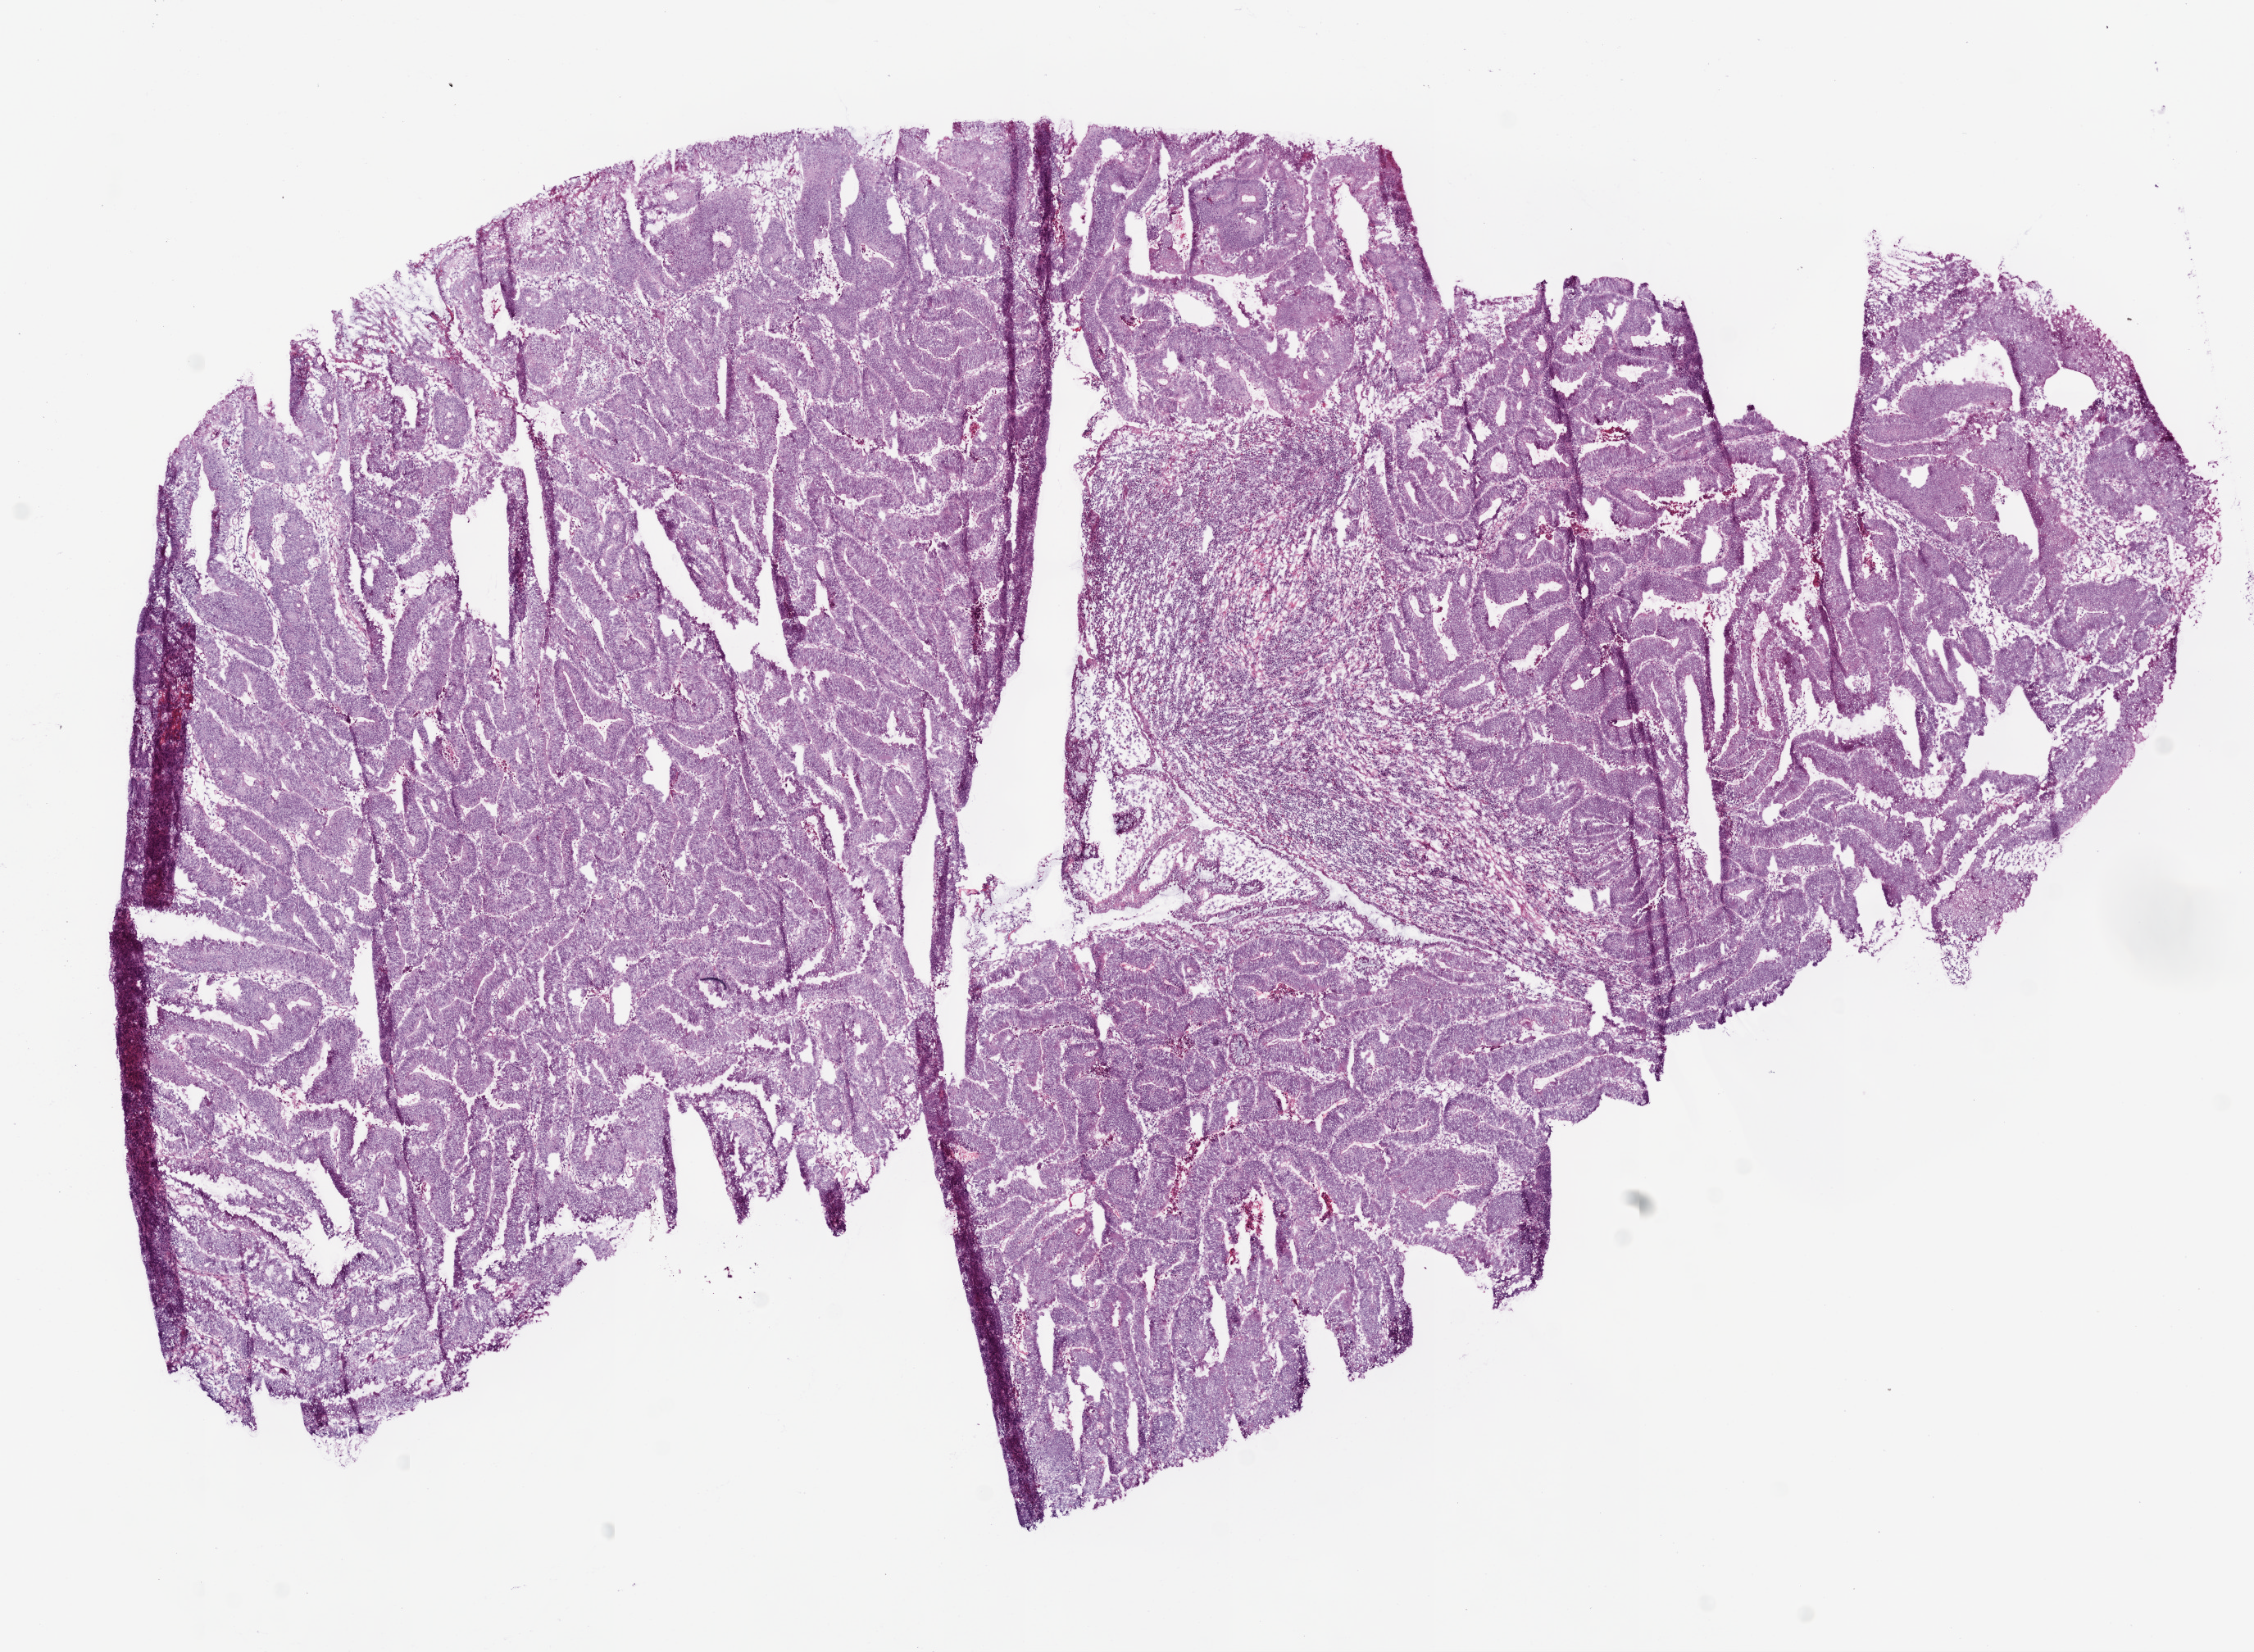
Whole-slide histology image, H&E-stained, a low-resolution overview of the entire scanned area, about 11.0 x 8.1 mm; frozen section from the top of the tissue portion; sample: primary tumour, rectum. Male patient; age at initial diagnosis 67 years. Slide review estimates, as recorded: tumour cells 88%, tumour nuclei 80%, normal cells 0%, stromal cells 2%, necrosis 10%.
* histologic diagnosis: Adenocarcinoma, NOS (rectosigmoid junction)
* lymph nodes positive (case pathology): 0 of 22 examined
* AJCC pathologic stage: I (5th edition)